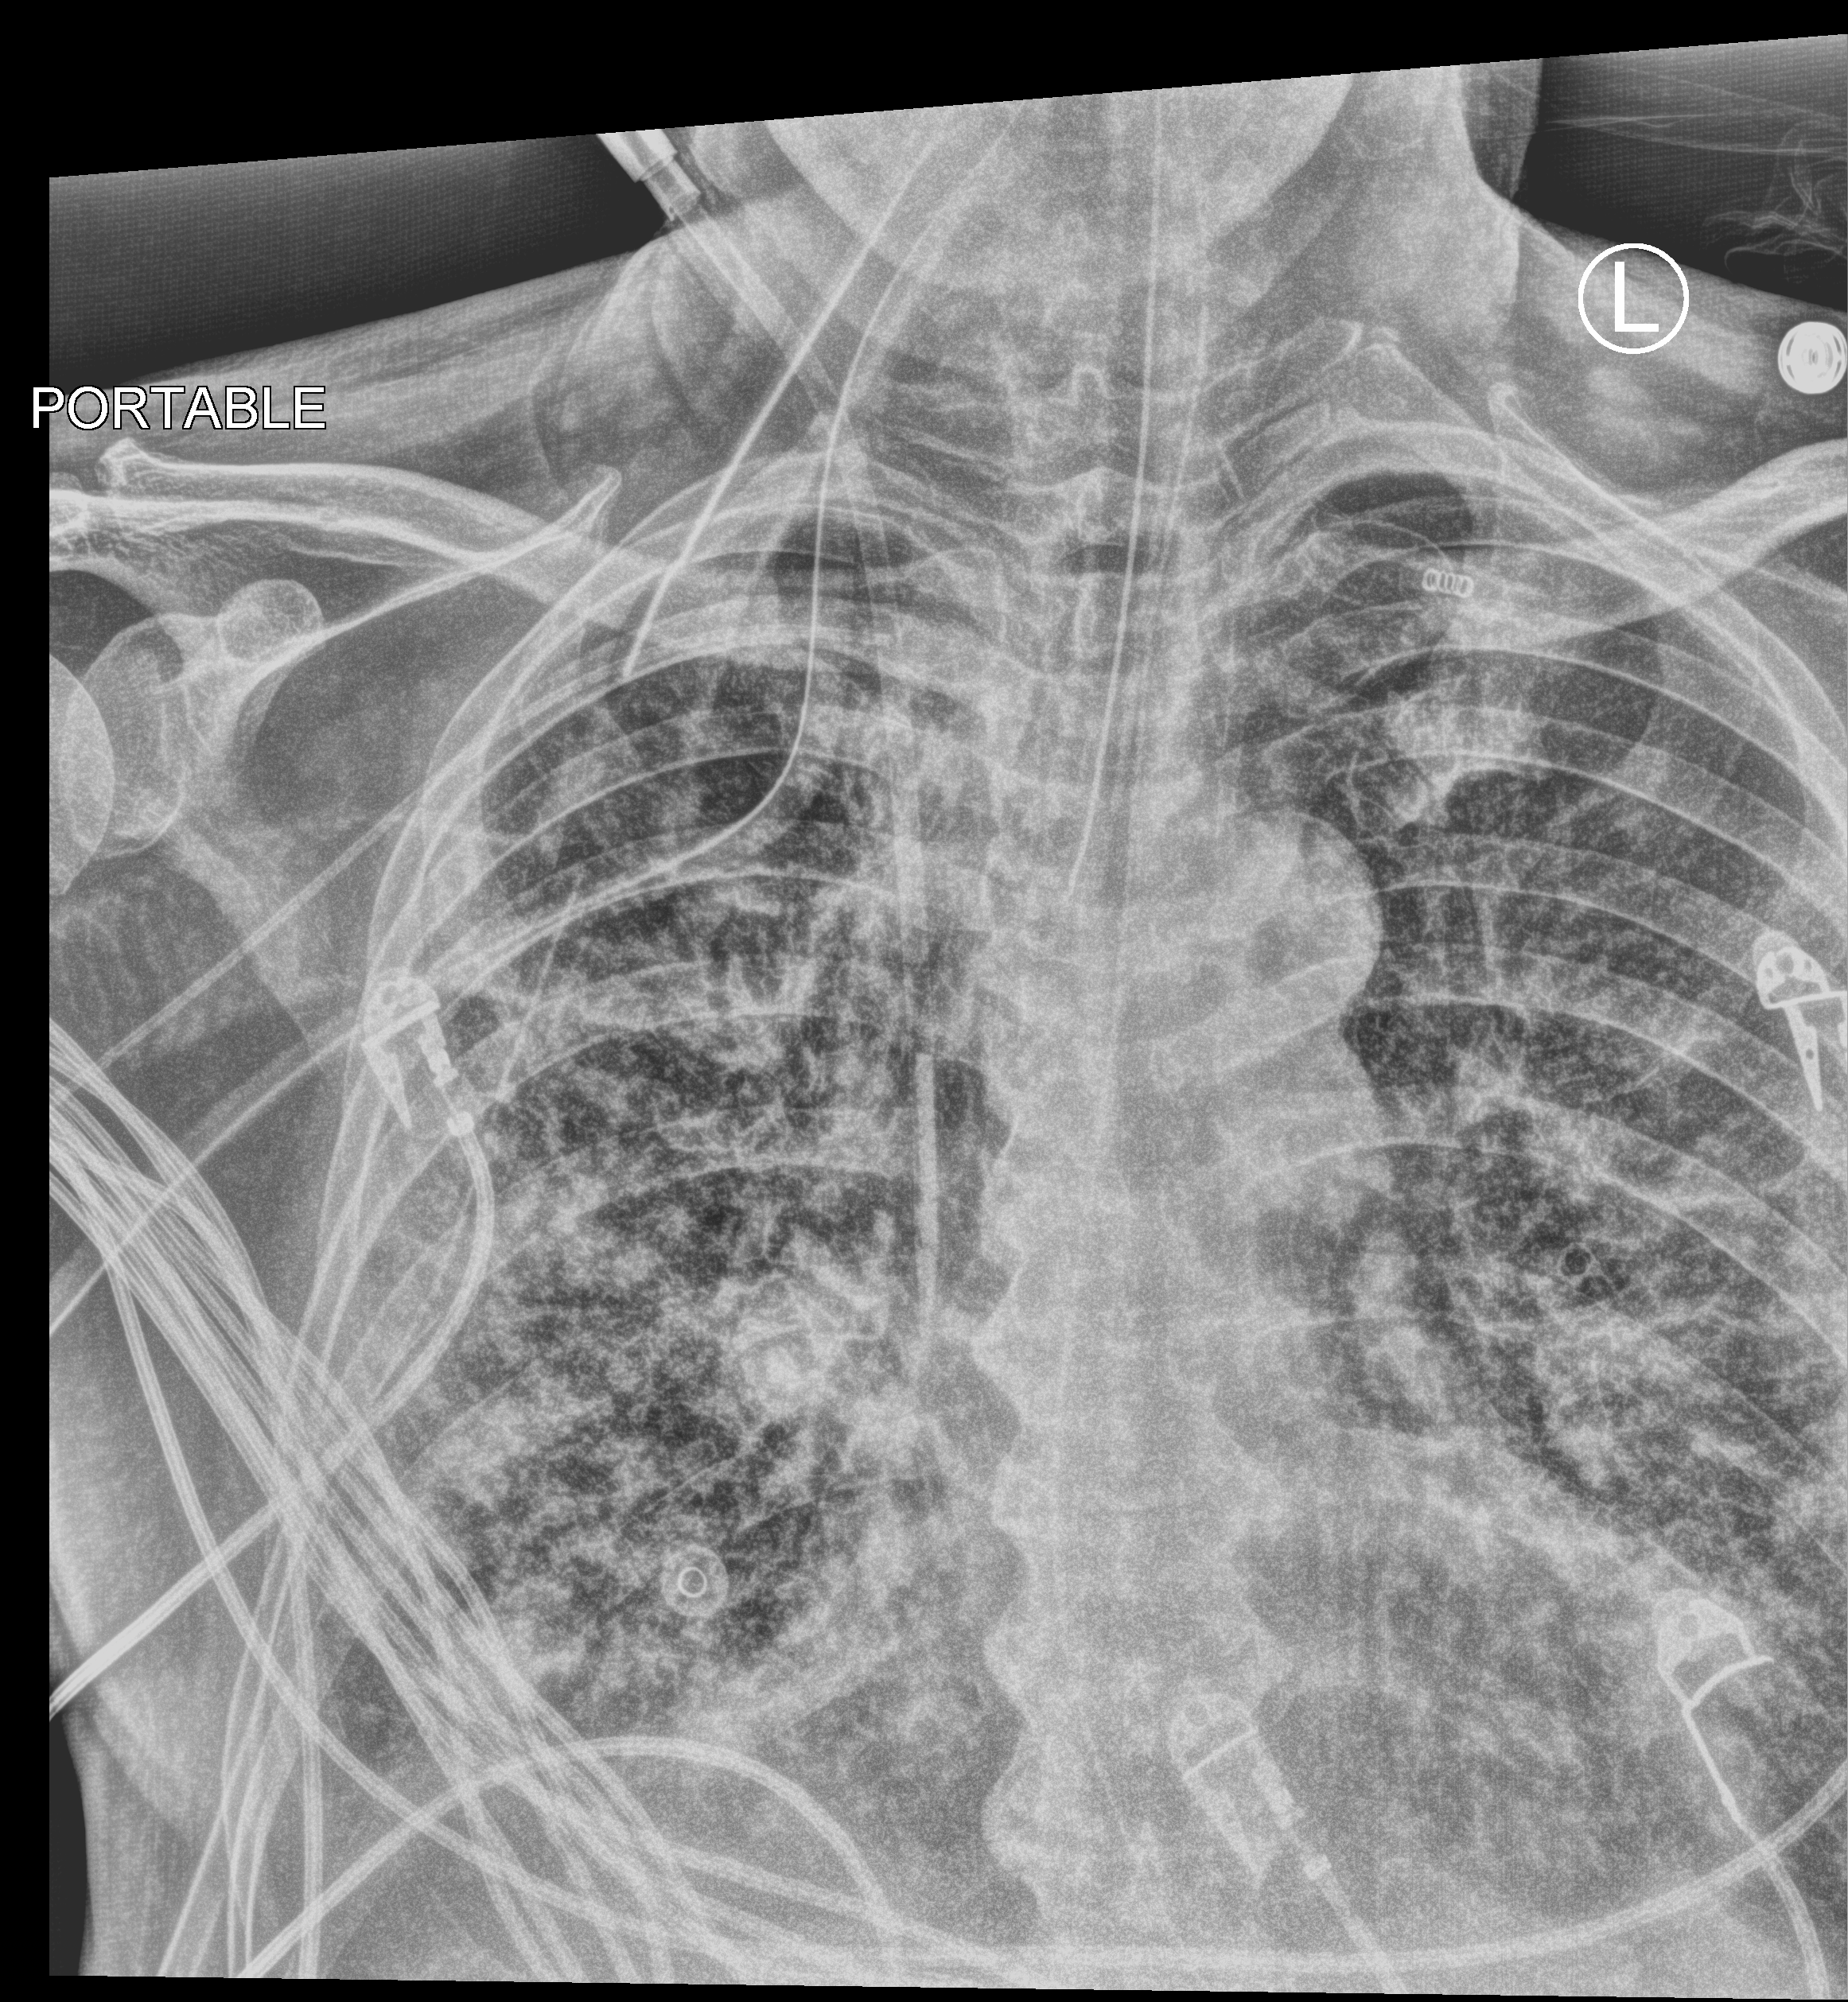
Portable chest radiograph; anteroposterior (AP) projection. Male patient hospitalised with COVID-19, age 60–74 years.
Admission-level facts for this patient (not findings on this image; timing relative to this image not recorded): mechanically ventilated during this hospital stay: yes.